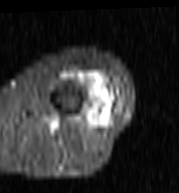
MRI of an extremity soft-tissue mass, one axial slice; position 31 of 103 along the scan axis; STIR; MR volume resampled by the dataset authors to the PET/CT grid (not the native acquisition matrix); 3.27 mm slice thickness; 179 × 193 image matrix, field of view 175 × 188 mm. Female patient. Case-level facts recorded for this patient, not image findings: histological type: undifferentiated – high grade; grade: high; site of the primary tumour: left thigh.
Structures marked on this image (expert contour drawn on MRI and transferred to this co-registered scan by the dataset authors):
- gross tumour volume including surrounding oedema: bounding box (x1, y1, x2, y2) in pixels: (63, 71, 117, 116)